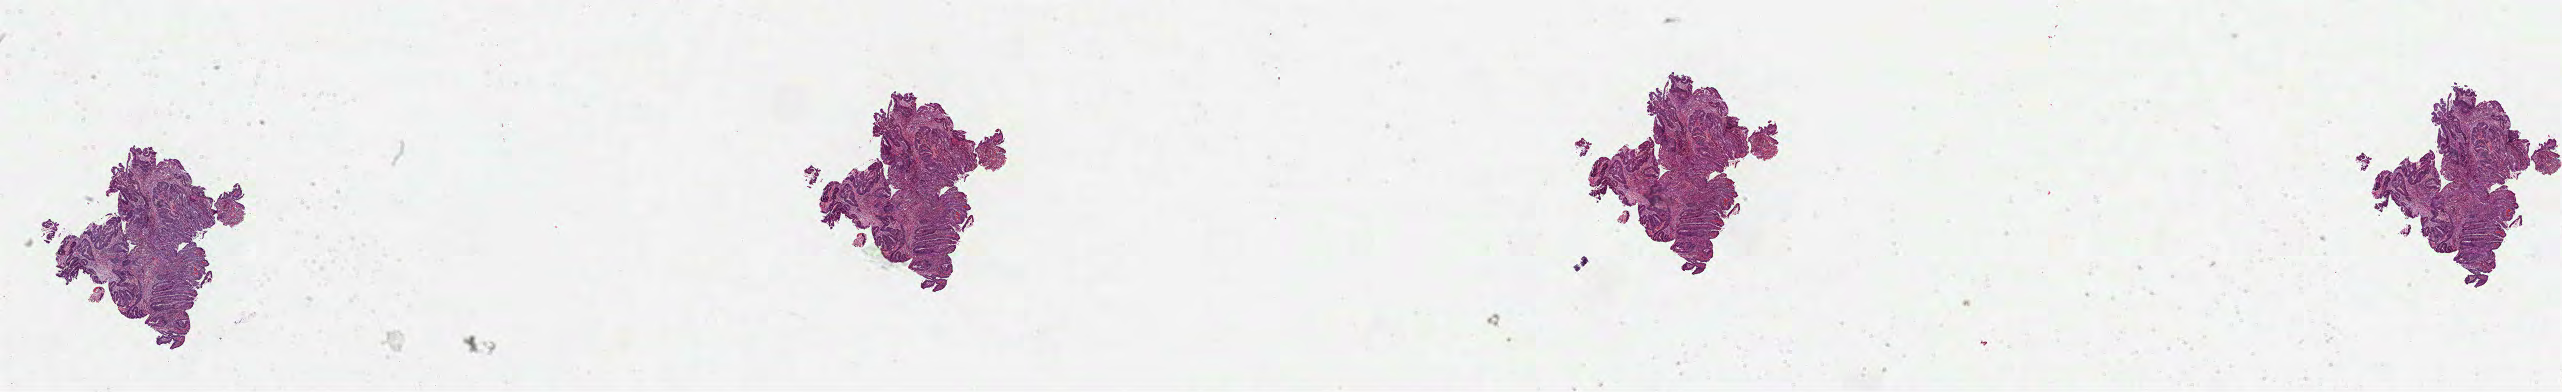
Digitized H&E tissue section (whole slide), a low-resolution overview of the entire scanned area, about 41.3 x 6.3 mm (from a 40x scan). Formalin-fixed paraffin-embedded (FFPE) diagnostic section. Primary tumour sample from the colon. Male, age 74 years at initial diagnosis.
TNM: T2 N0 M0. AJCC pathologic stage: I. Lymph nodes positive (case pathology): 0 of 16 examined. Diagnosis: Adenocarcinoma, NOS (sigmoid colon).